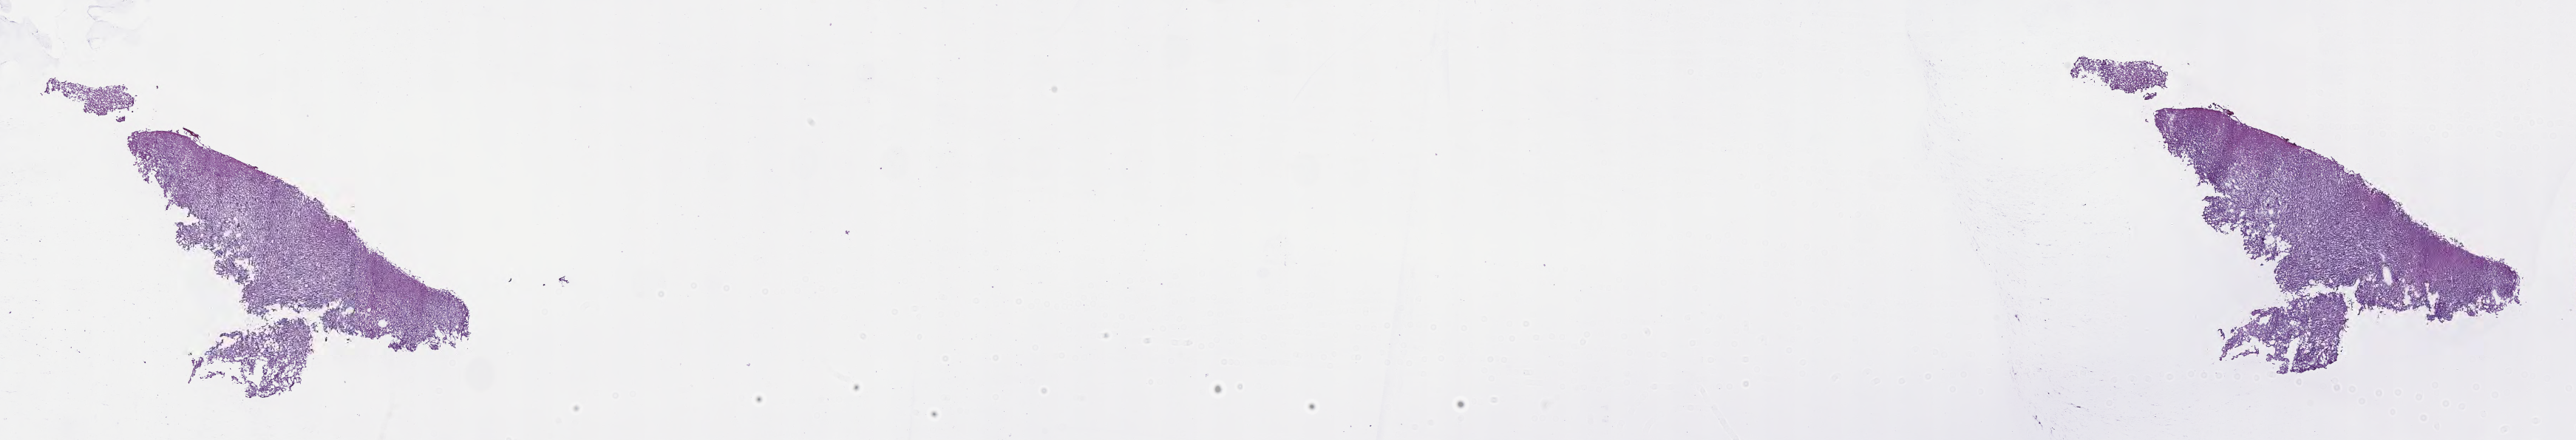
H&E whole-slide image of tumor tissue from the brain, shown as a low-resolution overview of the whole scanned area (about 28.2 x 4.8 mm). Cryosection (OCT / tissue freezing medium). Patient: male, age 211 months.
Diagnosis (ICD-O-3 morphology term): Dysembryoplastic neuroepithelial tumor.